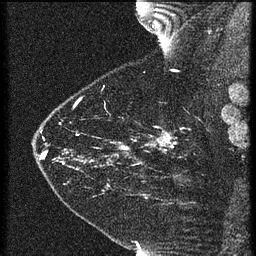
Breast MRI (dynamic contrast-enhanced), one sagittal slice. Slice 52 of 60 in the series (ordered by position). 3 images stored at this slice position (order not interpretable as contrast timing). 1.5 T. TE 4.2 ms, TR 21.3 ms. 256 × 256 image matrix, field of view 180 × 180 mm. Female patient, age 43 years. From the clinical record (not read from this slice): setting: breast cancer imaged before/during neoadjuvant chemotherapy; receptor status: HER2-positive.
Annotated regions visible in this slice (semi-automatically segmented with operator editing):
- analysis volume of interest (the breast-tissue region the enhancement analysis was run in; not a lesion): box from (x=119, y=114) to (x=189, y=173) px
- tumour enhancement mask (voxels above the 90 % enhancement threshold inside the analysis volume of interest): (x=126, y=132)–(x=175, y=149)